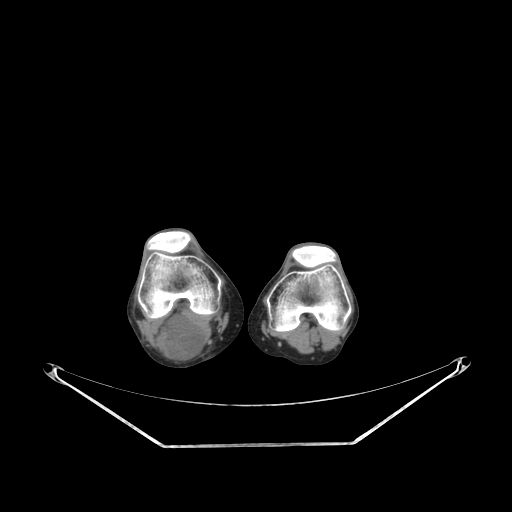
CT of an extremity soft-tissue mass (from a PET/CT study), one axial slice; position 167 of 267 along the scan axis; reconstruction kernel SOFT; 140 kVp; soft-tissue window (W 400 / L 40 HU); 3.75 mm slice thickness; 512 × 512 image matrix, field of view 500 × 500 mm. Female patient. Case-level facts recorded for this patient, not image findings: histological type: liposarcoma; site of the primary tumour: right thigh.
Structures marked on this image (expert contour drawn on MRI and transferred to this co-registered scan by the dataset authors):
- gross tumour volume (mass): bounding box [x1, y1, x2, y2] px = [155, 313, 204, 359]